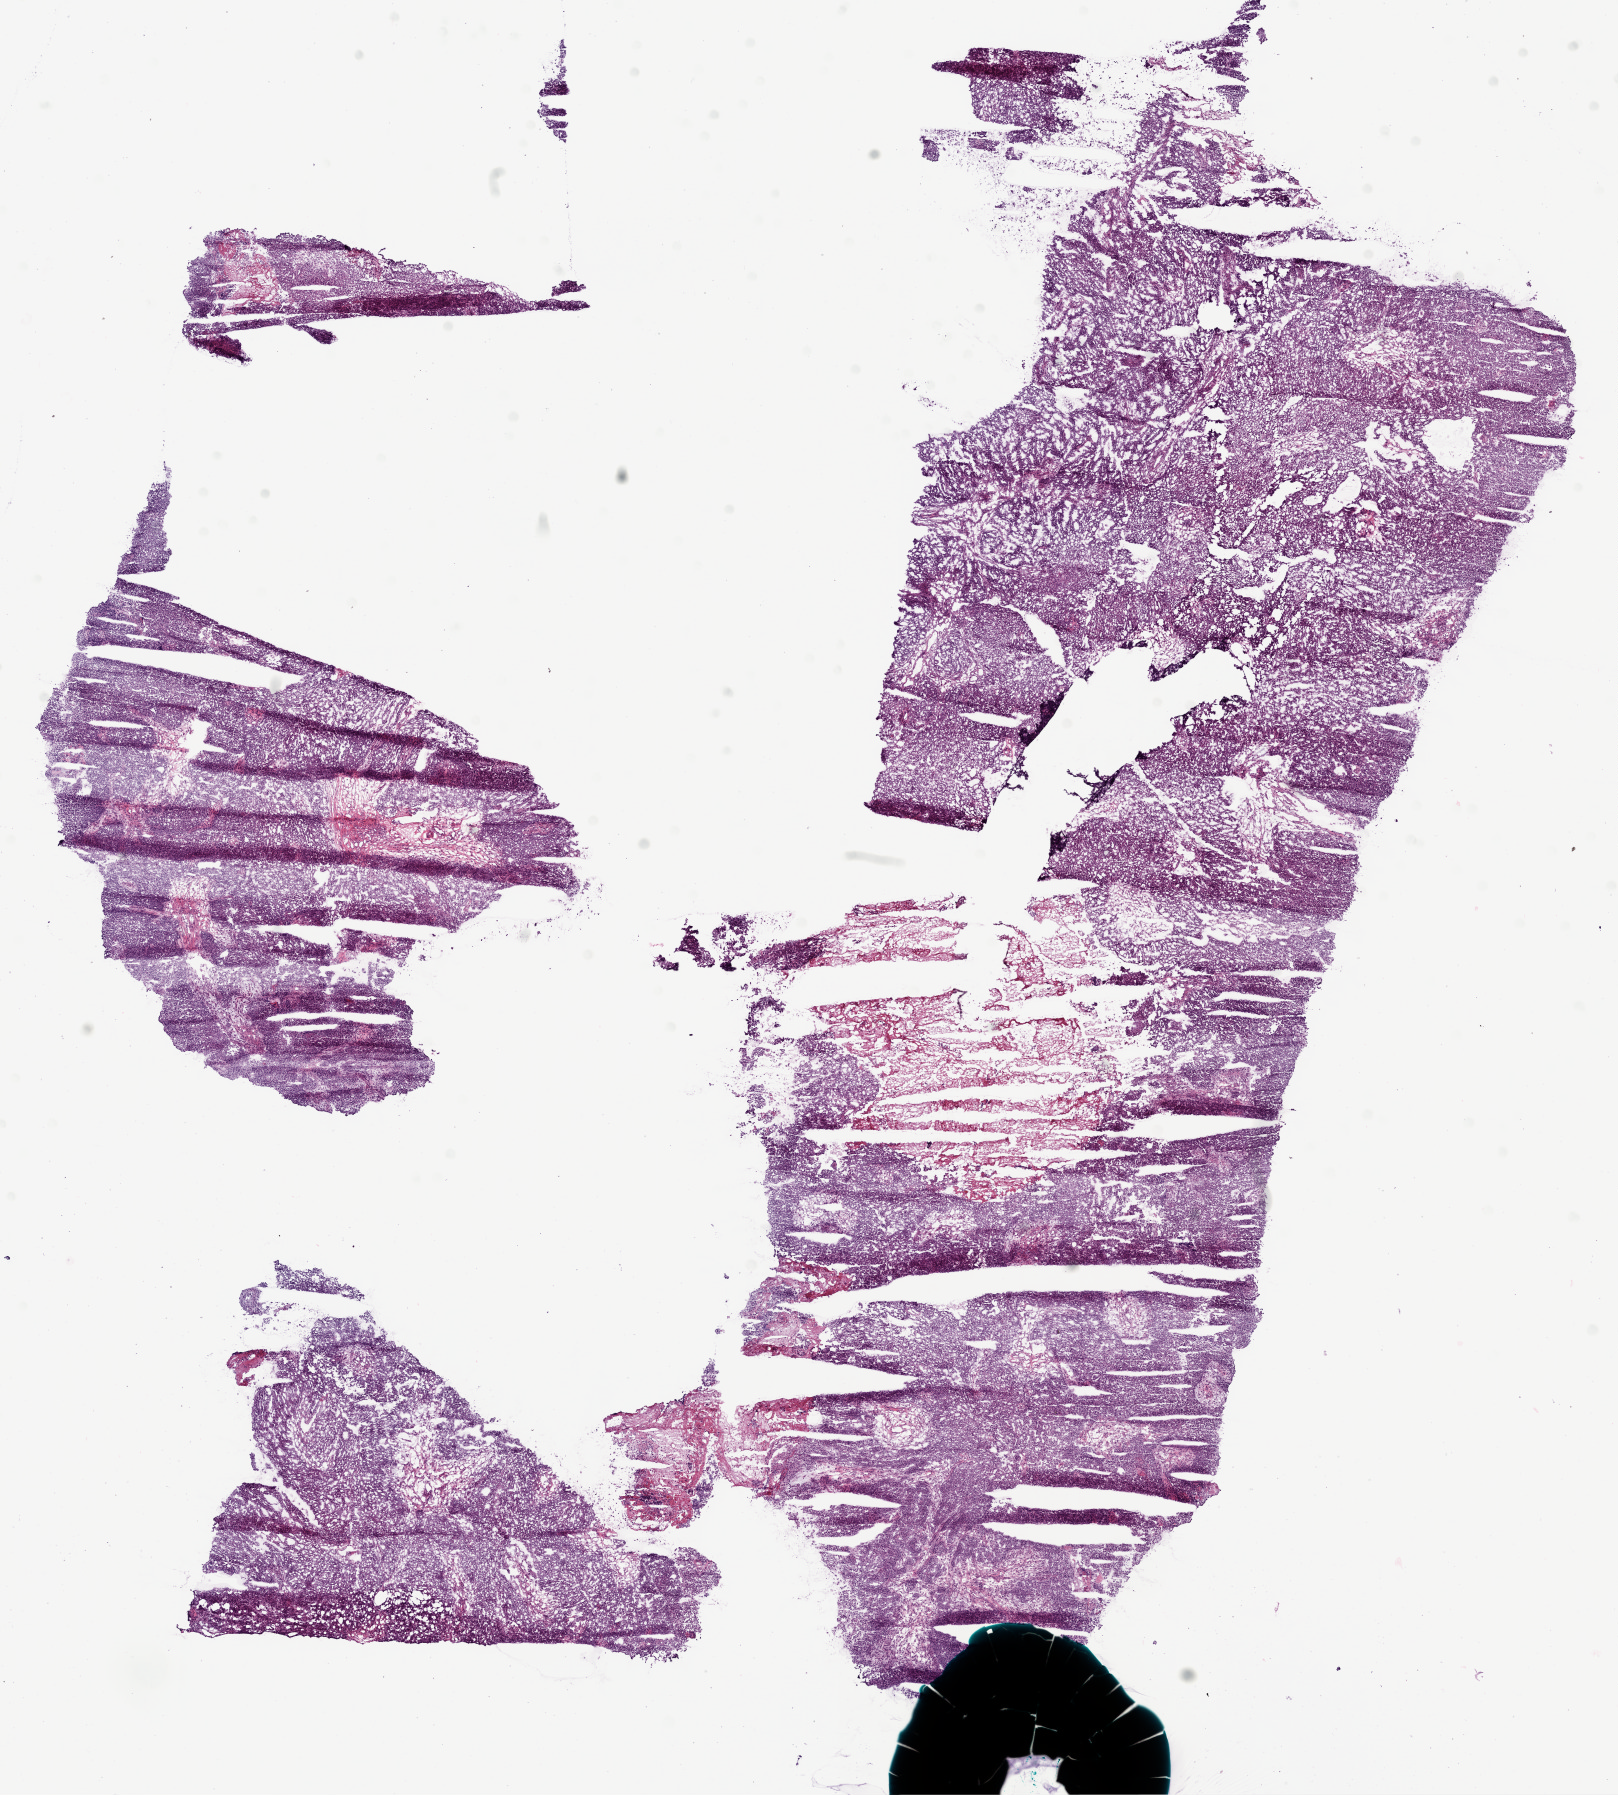
Whole-slide histology image, H&E-stained — low-resolution overview of the scanned area, about 13.1 x 14.5 mm, frozen section, sample: primary tumour, ovary. Female patient; age at initial diagnosis 52 years. Histologic grade: G3 (poorly differentiated). Pathologist review of this section (percent, as recorded): tumour cells 90%, tumour nuclei 95%, normal cells 0%, stromal cells 10%, necrosis 0%.
FIGO stage: IIIC. Laterality: bilateral. Histologic diagnosis: Serous cystadenocarcinoma, NOS.